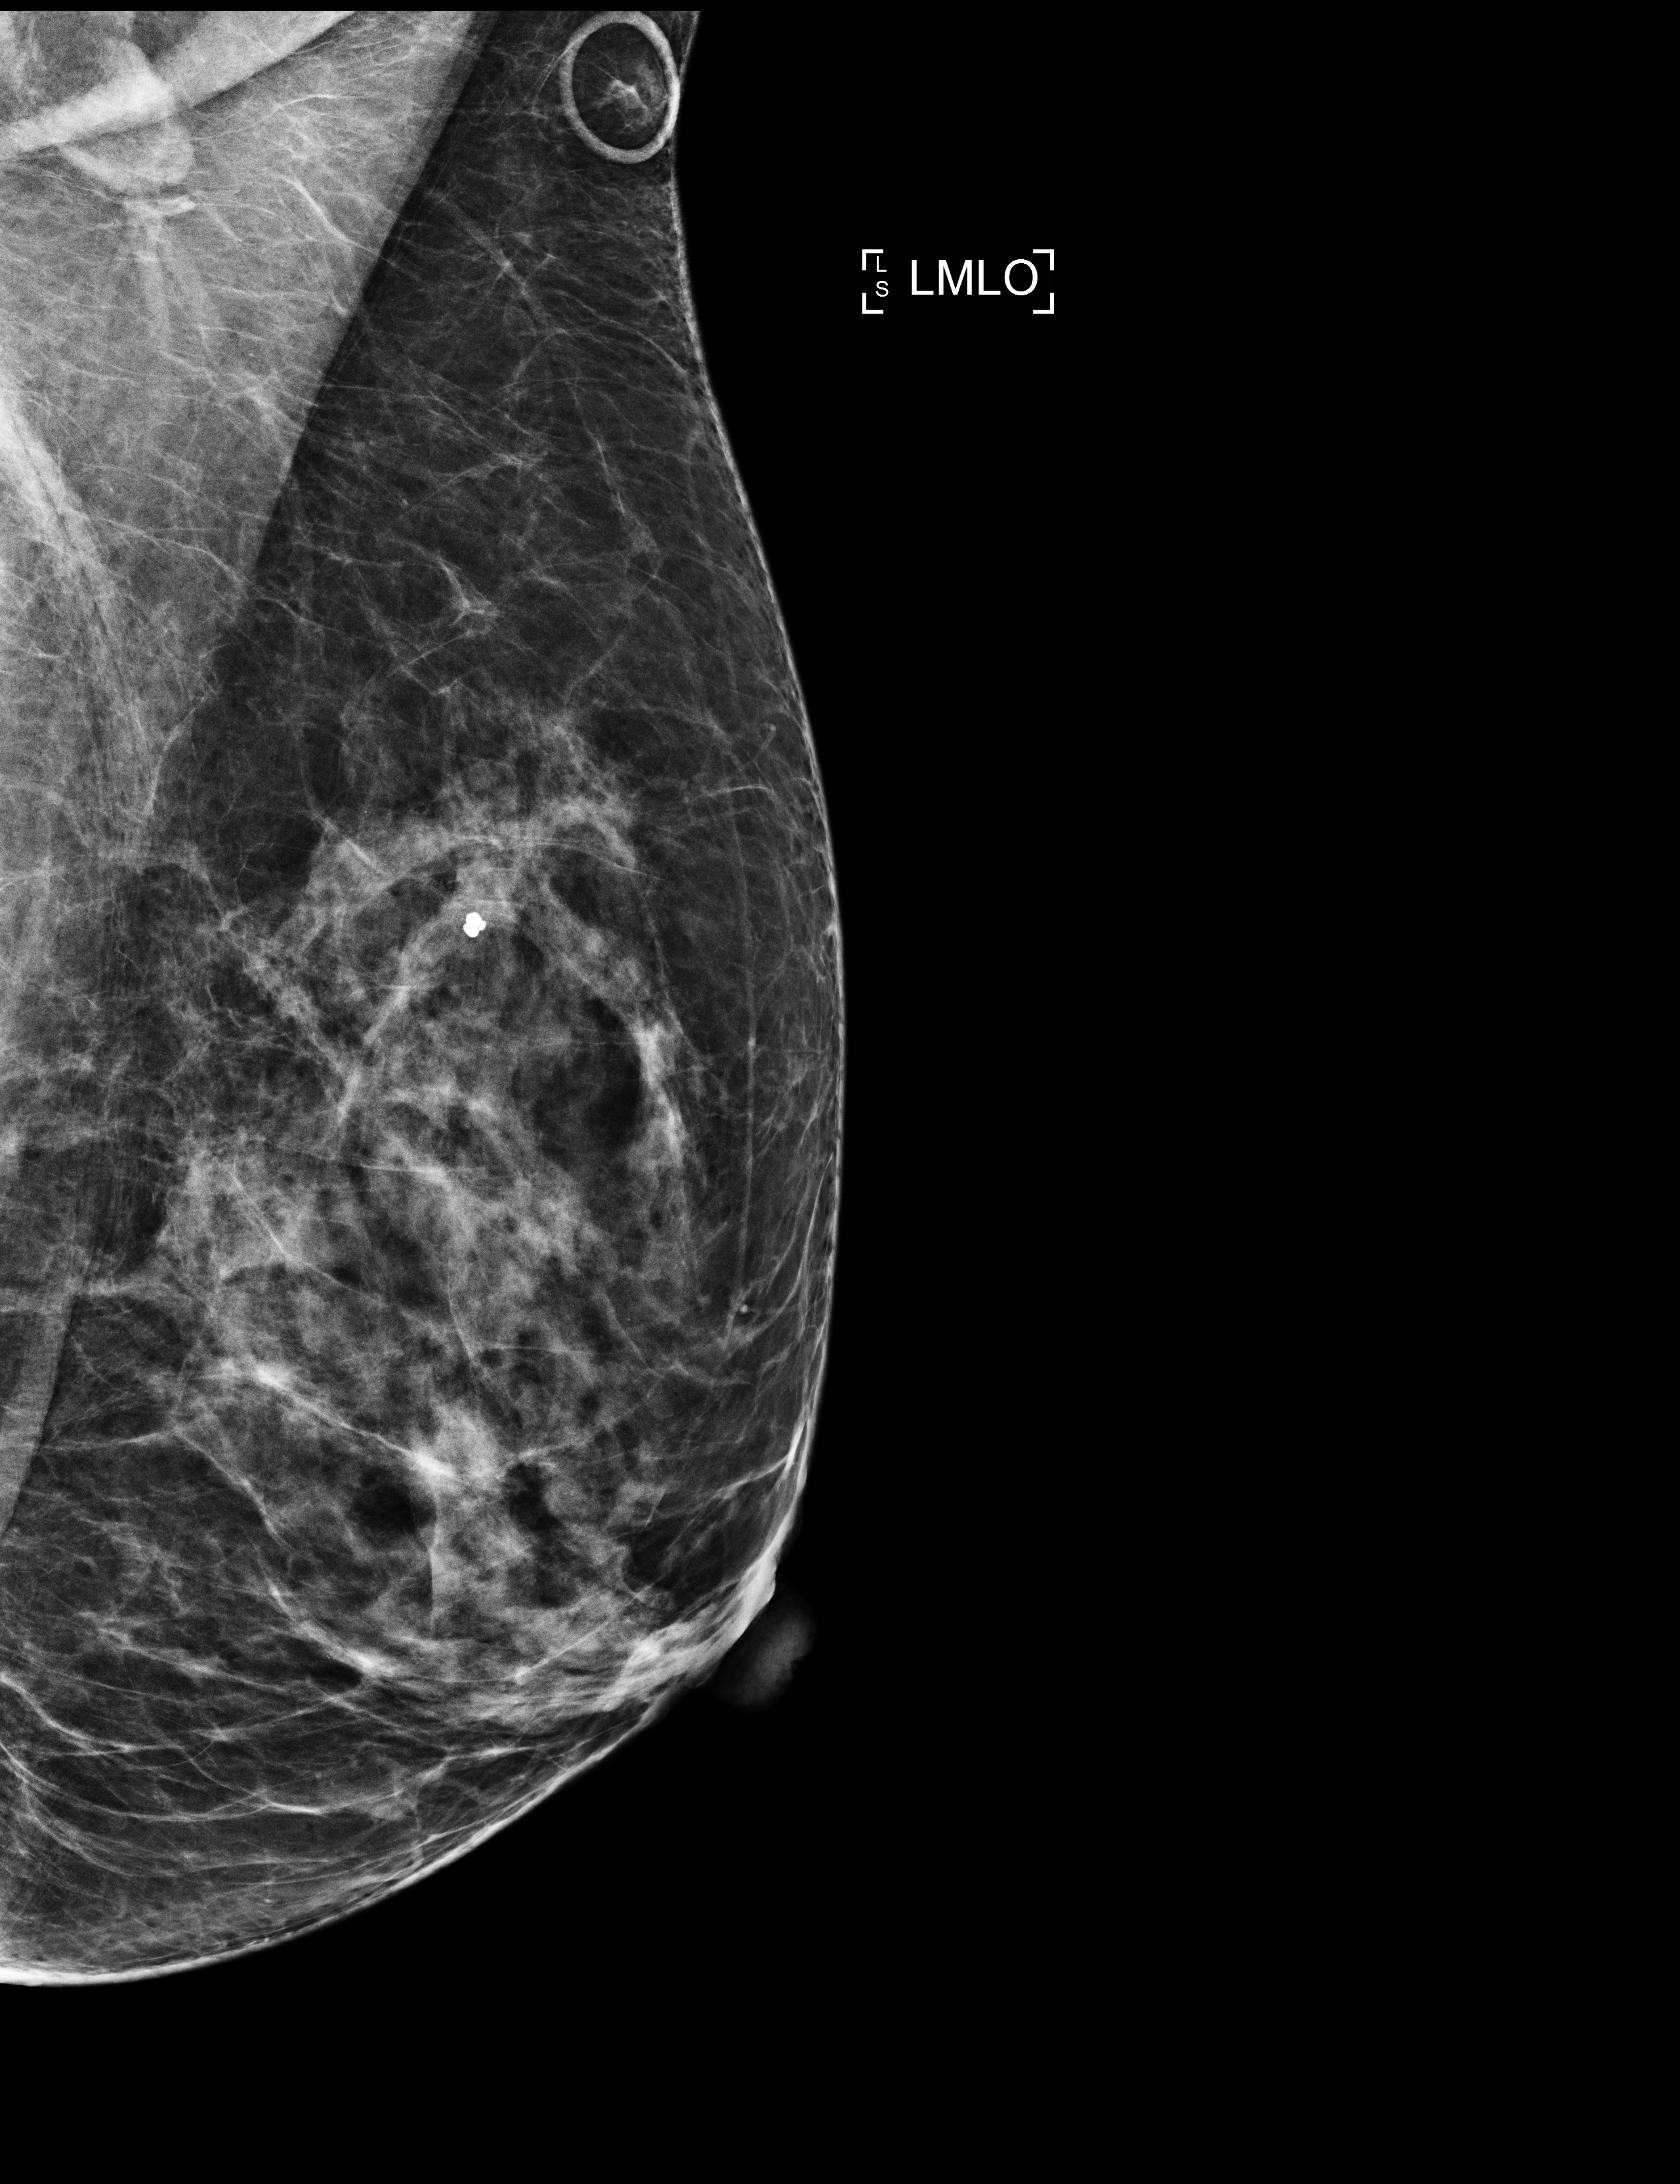
Screening examination. Female patient, age 61 years.
Image type: full-field digital mammogram. Breast: left. Projection: MLO view.